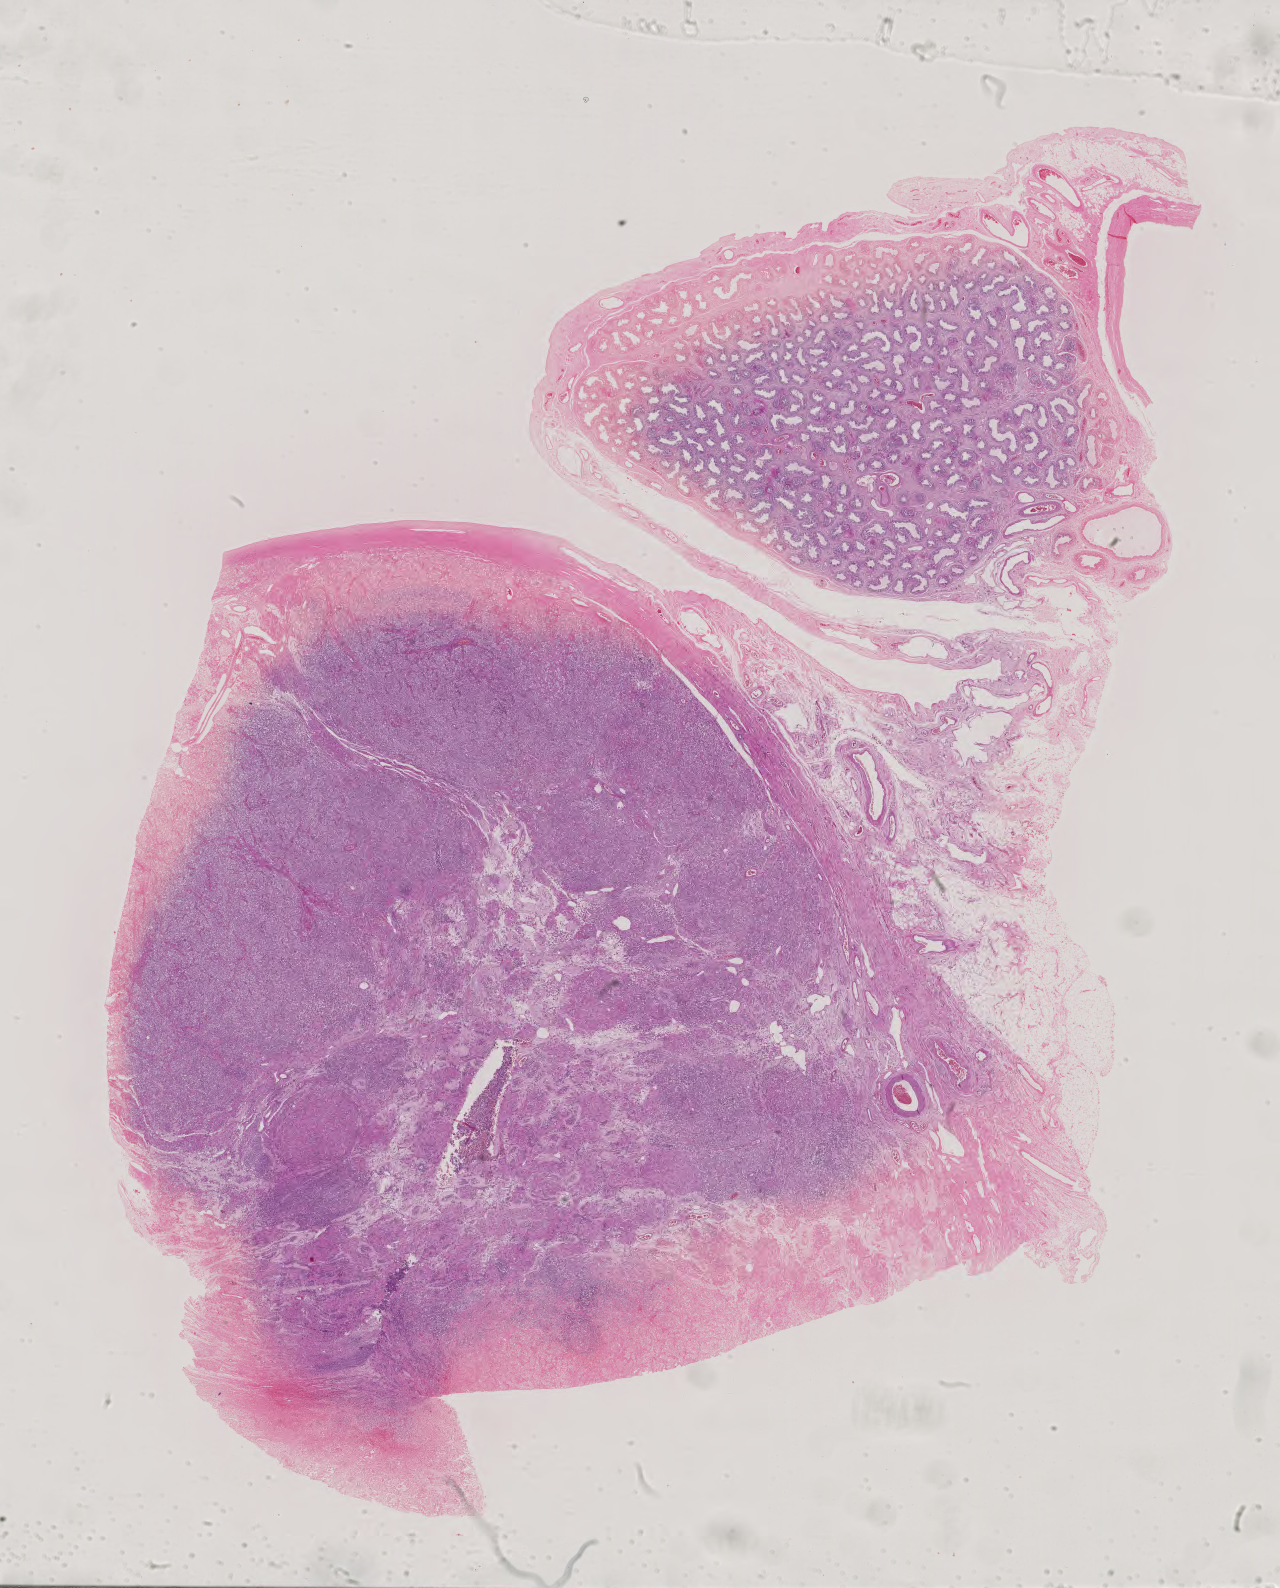
Whole-slide histology image, H&E — shown as a low-resolution overview of the whole scanned area (about 18.7 x 23.1 mm); formalin-fixed paraffin-embedded (FFPE) diagnostic section; primary tumour sample from the testis. Male, age 31 years at initial diagnosis.
AJCC pathologic stage: IS (5th edition). Diagnosis: Seminoma, NOS.